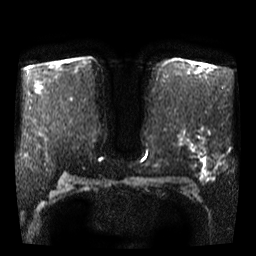
Breast MRI, one axial slice. Diffusion-weighted series; image 2 of 4 stored at this slice position (different b-values; order by instance number). 3 T. 5 mm slice thickness. 256 × 256 image matrix. Female patient.
Annotated regions visible in this slice (expert manual segmentation):
- tumour on diffusion-weighted imaging: box from (x=200, y=156) to (x=209, y=162) px